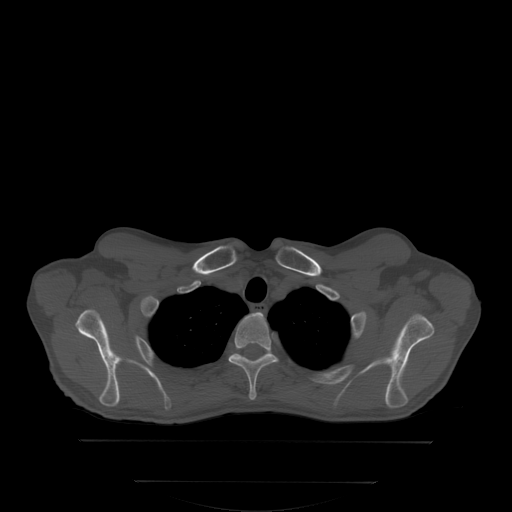
CT including the spine, one axial slice. Slice 277 of 350 in the series (ordered by position). Bone window (W 1800 / L 400 HU). 2.5 mm slice thickness. 512 × 512 image matrix, field of view 500 × 500 mm. Male patient, age 58 years. Case-level facts recorded for this patient, not image findings: primary cancer: prostate; vertebrae with lytic lesions (as recorded): L1.
Annotated regions visible in this slice (semi-automatically segmented with operator editing):
- T2 vertebra: box from (x=232, y=314) to (x=279, y=400) px
- T3 vertebra: (x=228, y=351)–(x=273, y=362)